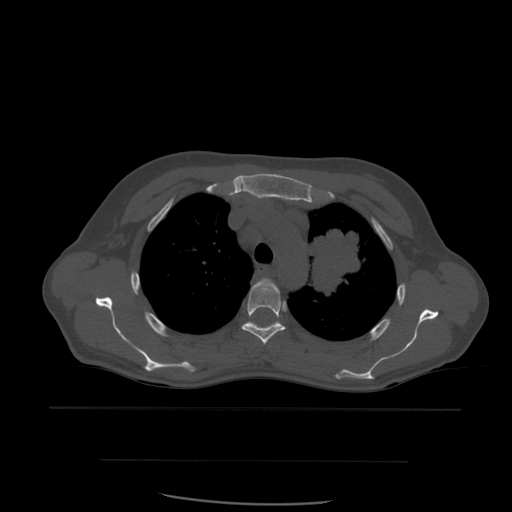
CT including the spine, one axial slice; position 427 of 574 along the scan axis; bone window (W 1800 / L 400 HU); 1.25 mm slice thickness; 512 × 512 image matrix, field of view 392 × 392 mm. Patient age 48 years. From the clinical record (not read from this slice): primary cancer: lung; vertebrae with lytic lesions (as recorded): T11.
Annotated regions visible in this slice (semi-automatically segmented with operator editing):
- T3 vertebra: bounding box <254,280,270,289> (left, top, right, bottom; pixels)
- T4 vertebra: <242,281,286,345>
- T5 vertebra: <249,322,276,324>